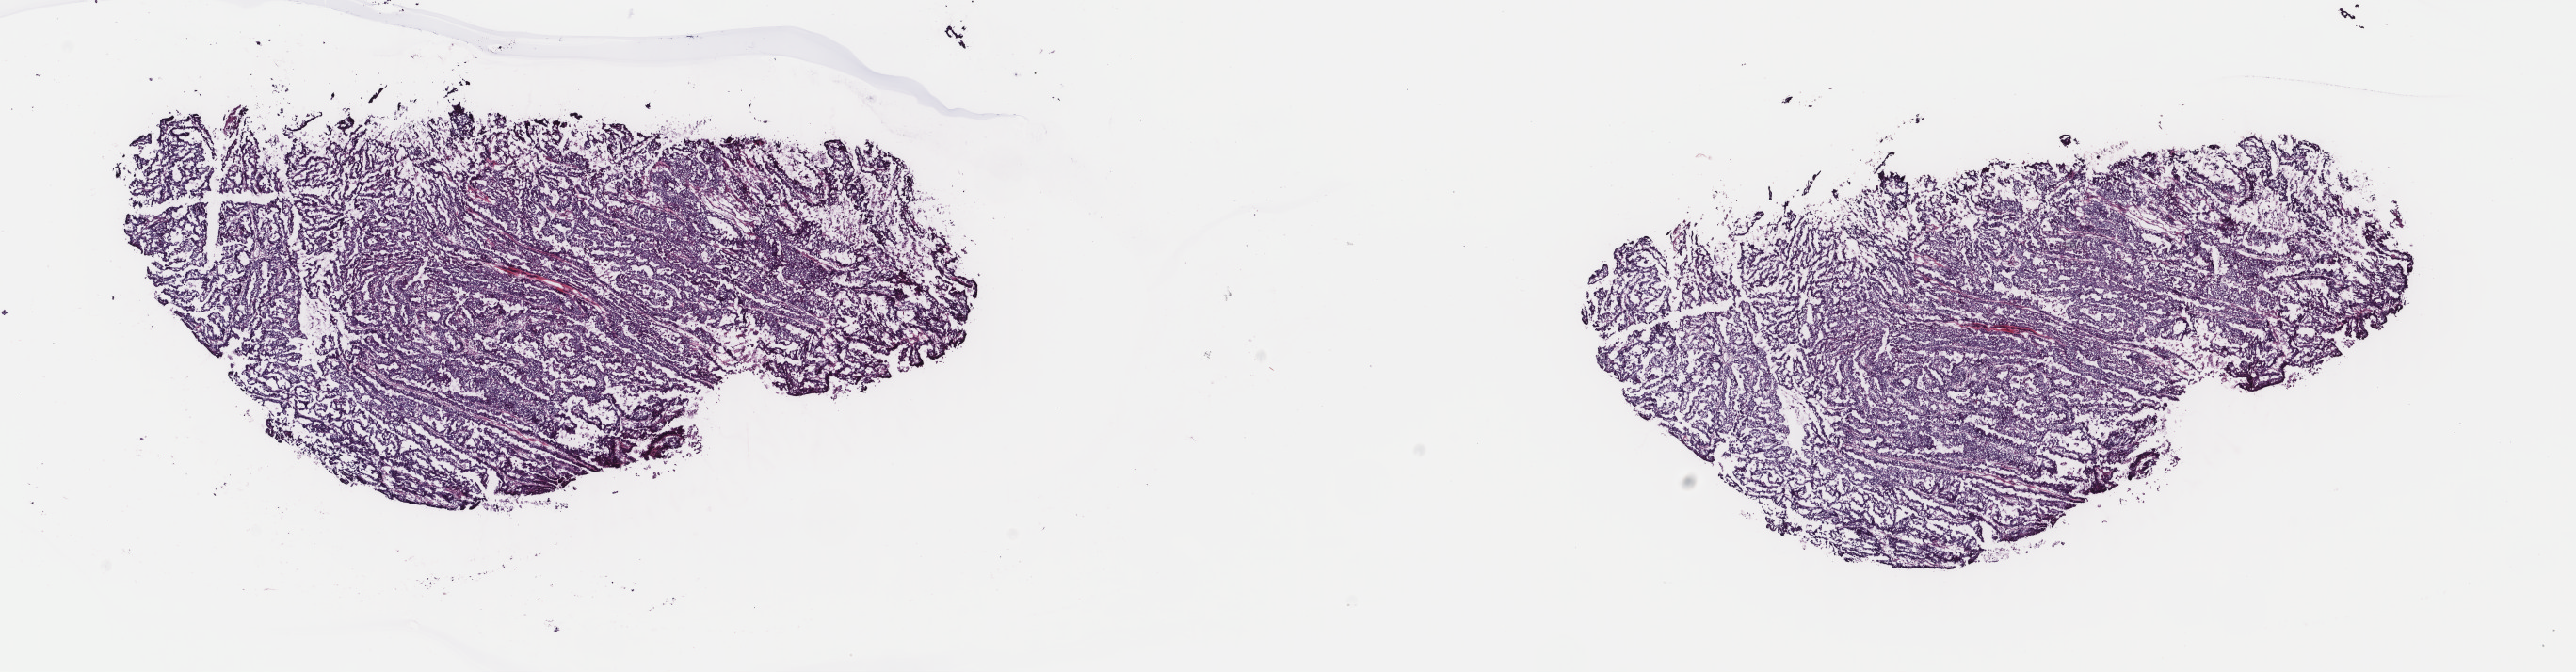
Digitized Hematoxylin and eosin (H&E) stained tissue section (whole slide), shown as a low-resolution overview of the whole scanned area (about 21.7 x 5.7 mm), frozen section from the top of the tissue portion, primary tumour sample from the uterus. Female patient; age at initial diagnosis 73 years. Histologic grade: G3 (poorly differentiated). Composition of this section per pathologist review: tumour cells 100%, tumour nuclei 85%, normal cells 0%, stromal cells 0%, necrosis 0%. Infiltration values recorded for this section: lymphocyte infiltration 0%, monocyte infiltration 0%, neutrophil infiltration 0%.
FIGO stage: IVB. Histologic diagnosis: Serous cystadenocarcinoma, NOS.